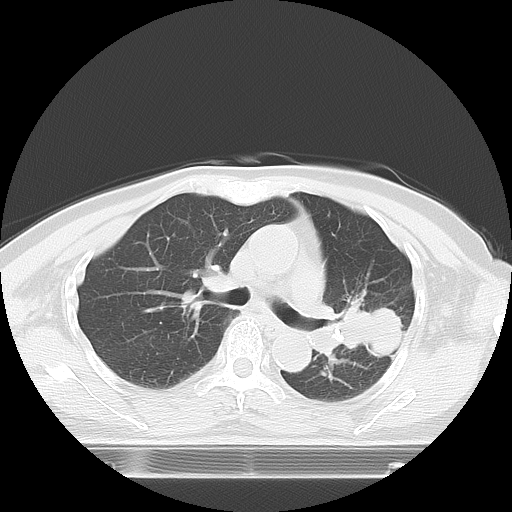
Chest CT, one axial slice. Position 2 of 21 along the scan axis. 120 kVp. Lung window (W 1500 / L -600 HU). 5 mm slice thickness. 512 × 512 image matrix, field of view 350 × 350 mm. Female patient, age 74 years. Case-level facts recorded for this patient, not image findings: clinical TNM (as recorded): T3 N1 M1c; histopathological grade: G3.
Structures marked on this image (rectangle marked by the reading radiologist):
- lung tumour (recorded histology: small cell carcinoma): box from (x=329, y=295) to (x=408, y=362) px